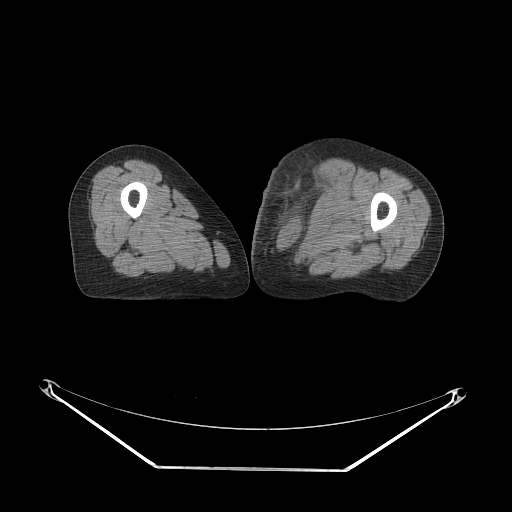
CT of an extremity soft-tissue mass (from a PET/CT study), one axial slice. Position 45 of 91 along the scan axis. Reconstruction kernel STANDARD. 140 kVp. Soft-tissue window (W 400 / L 40 HU). 512 × 512 image matrix, field of view 500 × 500 mm. Female patient. From the clinical record (not read from this slice): histological type: pleomorphic leiomyosarcoma; grade: high; site of the primary tumour: left thigh.
Annotated regions visible in this slice (expert contour drawn on MRI and transferred to this co-registered scan by the dataset authors):
- gross tumour volume including surrounding oedema: bounding box (x1, y1, x2, y2) in pixels: (263, 164, 339, 238)
- gross tumour volume (mass): (304, 190, 321, 200)